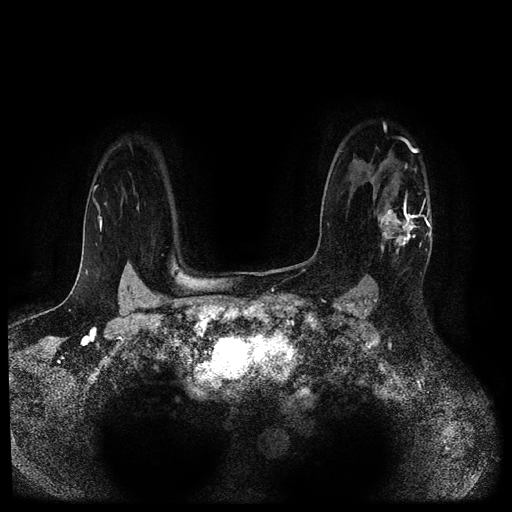
Breast MRI (dynamic contrast-enhanced, multi-phase), one axial slice; position 79 of 116 along the scan axis; dynamic contrast-enhanced series, time point 2 of 5 at this slice position (early post-contrast); 1.5 T; TE 2.7 ms, TR 5.4 ms; 2.2 mm slice thickness; 512 × 512 image matrix. Female patient, age 43 years.
Outlined on this slice (semi-automatically segmented with operator editing):
- breast lesion (labelled 'tumour' in the annotation; benign lesions carry a separate 'benign' label): bounding box <374,197,422,260> (left, top, right, bottom; pixels)